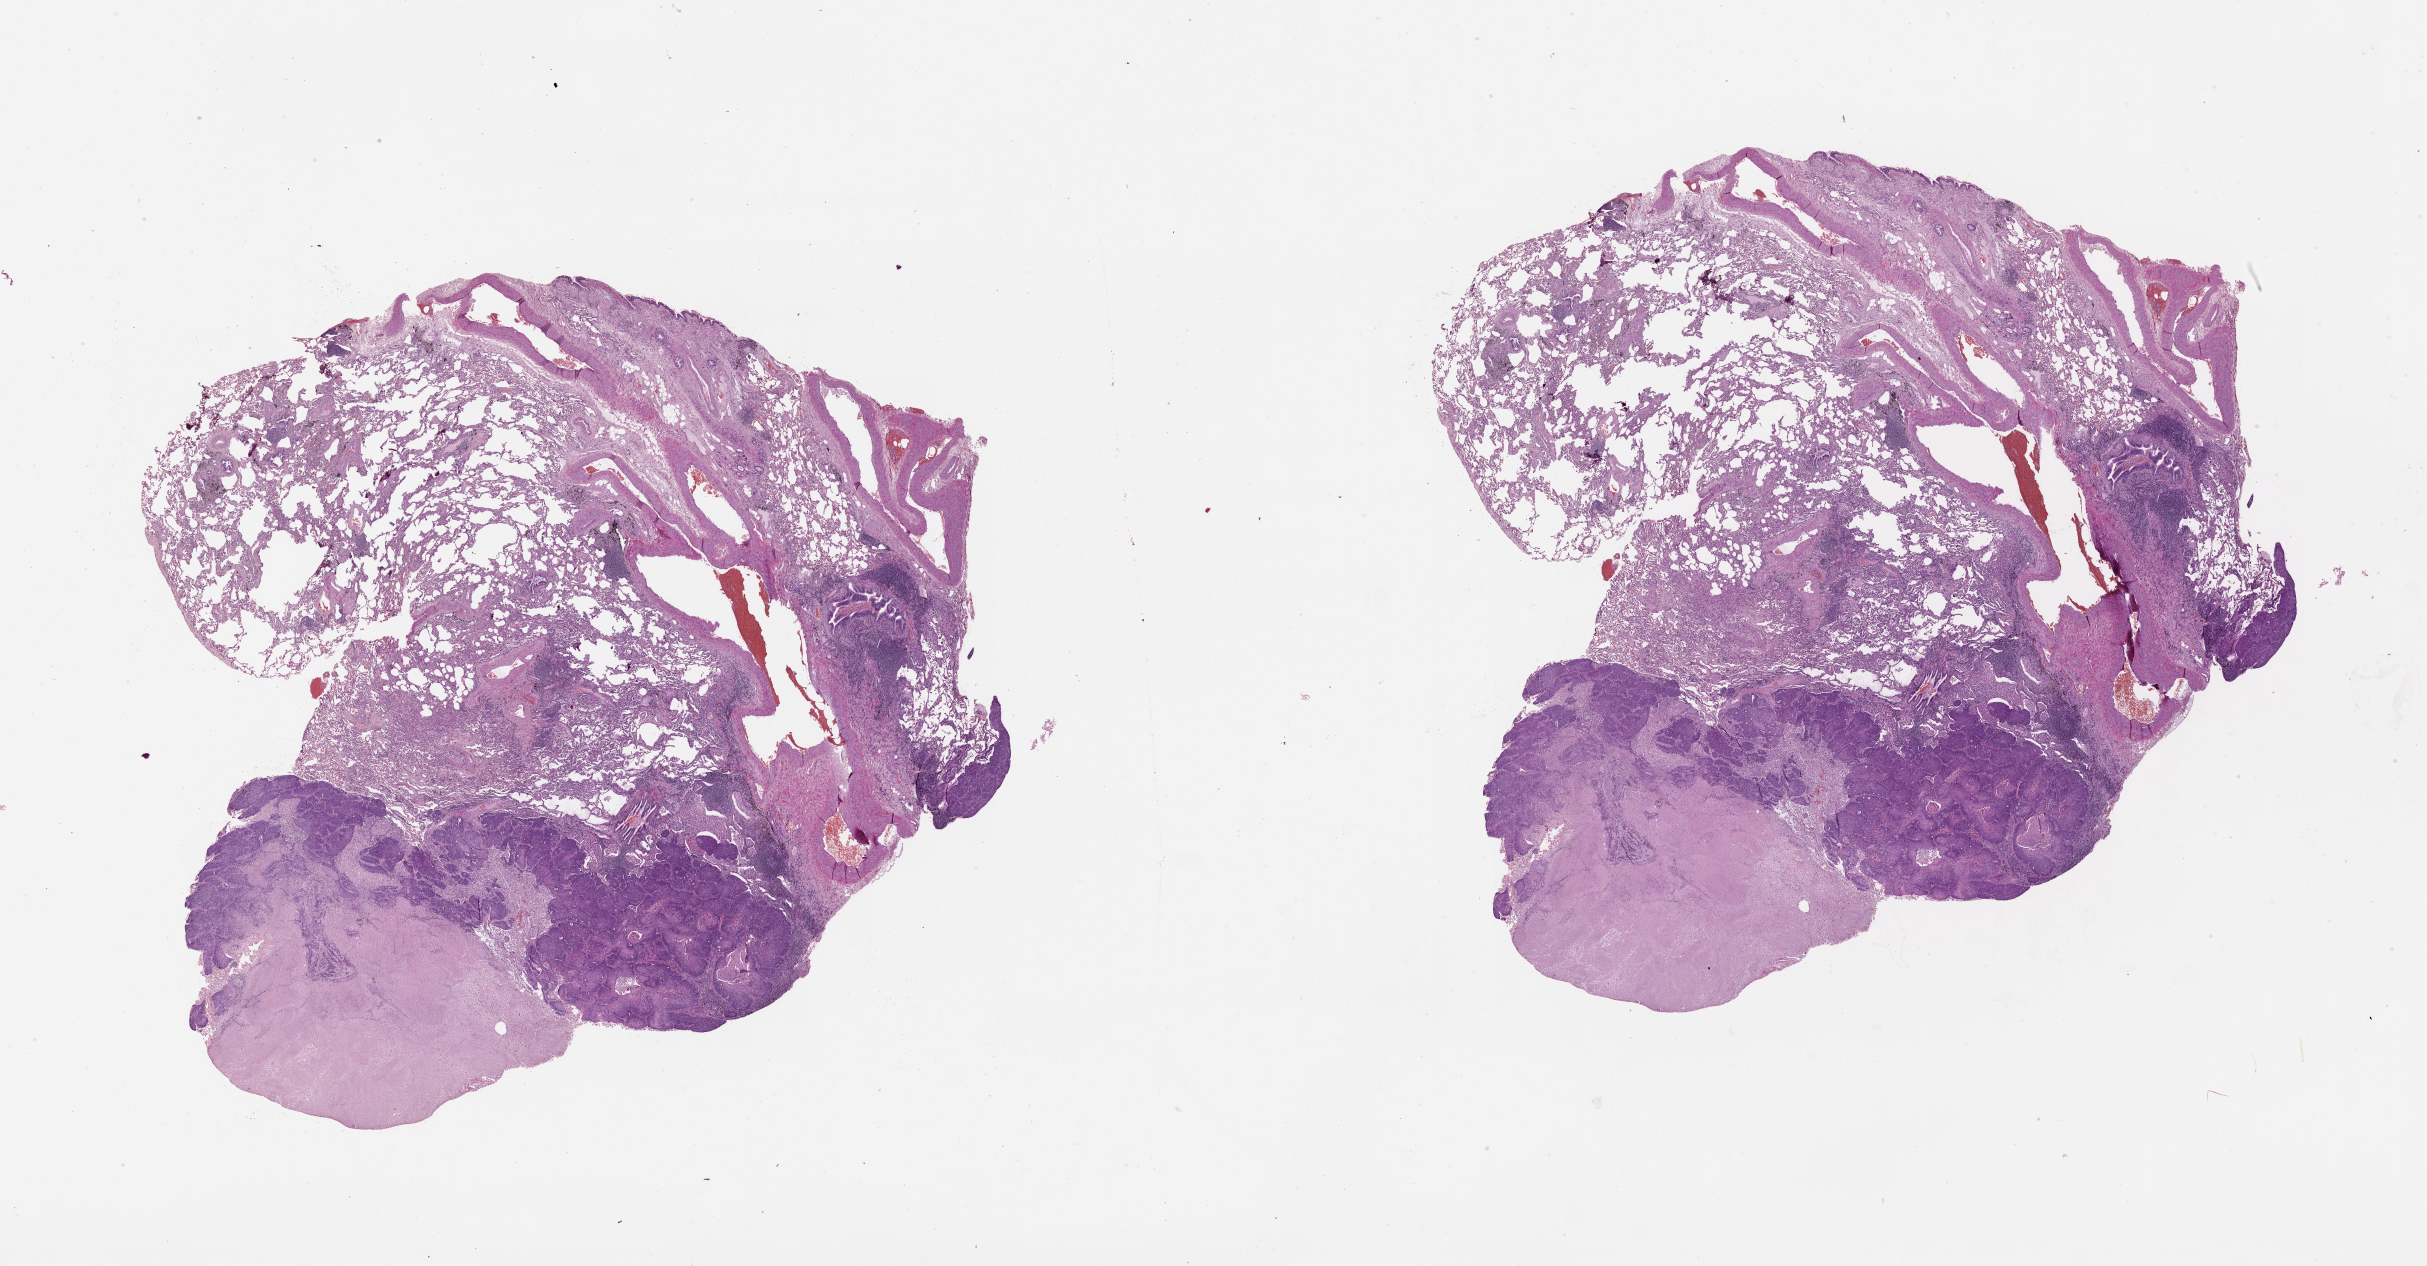
H&E-stained whole-slide image, a low-resolution overview of the entire scanned area, about 39.1 x 20.4 mm, tumour tissue sample, lung. Patient: female, age 60 years.
Patient diagnosis (cohort enrolment): squamous cell carcinoma (lung).